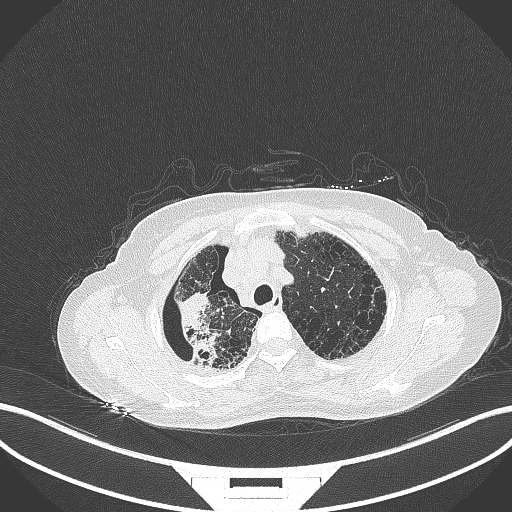
Chest CT, one axial slice. Position 293 of 408 along the scan axis. Lung window (W 1500 / L -600 HU). 512 × 512 image matrix. Female patient, age 64 years. Case-level facts recorded for this patient, not image findings: clinical TNM (as recorded): T3 N3 M0.
Annotated regions visible in this slice (bounding box drawn by a radiologist):
- lung tumour (recorded histology: squamous cell carcinoma): bounding box (x1, y1, x2, y2) in pixels: (173, 287, 223, 371)